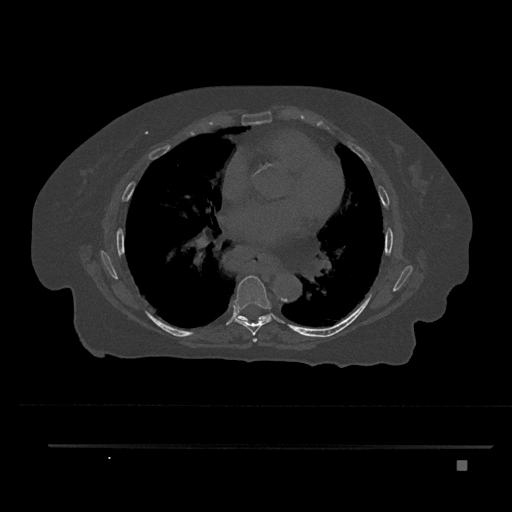
CT including the spine, one axial slice. Slice 475 of 797 in the series (ordered by position). Reconstruction kernel Br40s/3. 120 kVp. Bone window (W 1800 / L 400 HU). 512 × 512 image matrix. Patient: female, 76 years. Case-level facts recorded for this patient, not image findings: primary cancer: lung.
Outlined on this slice (semi-automatic segmentation, software-assisted and operator-edited):
- T6 vertebra: box from (x=252, y=338) to (x=257, y=343) px
- T7 vertebra: (x=233, y=275)–(x=272, y=336)
- T8 vertebra: (x=236, y=313)–(x=270, y=321)